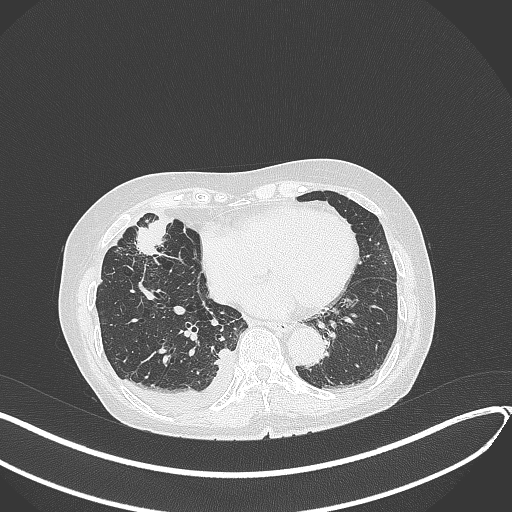
Chest CT, one axial slice. Reconstruction kernel B70f. Lung window (W 1500 / L -600 HU). 1 mm slice thickness. 512 × 512 image matrix. Female patient, age 75 years. Case-level facts recorded for this patient, not image findings: clinical TNM (as recorded): T2a N3 M0.
Annotated regions visible in this slice (rectangle marked by the reading radiologist):
- lung tumour (recorded histology: adenocarcinoma): bounding box <135,214,167,259> (left, top, right, bottom; pixels)